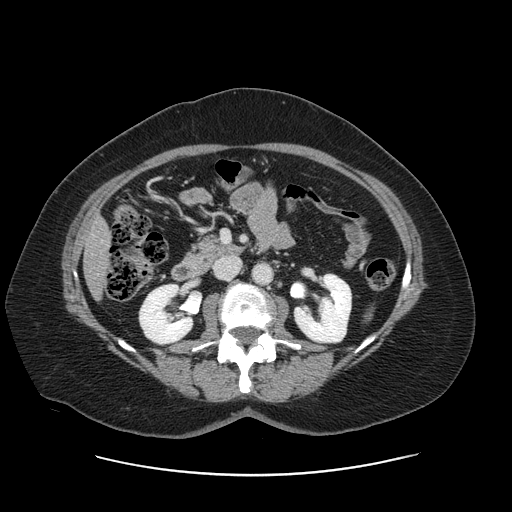
Contrast-enhanced abdominal CT, one axial slice. Slice 50 of 161 in the series (ordered by position). 120 kVp. Intravenous contrast given. Soft-tissue window (W 400 / L 40 HU). 2.5 mm slice thickness. 512 × 512 image matrix. Female patient, age 62 years. From the clinical record (not read from this slice): diagnosis: colorectal cancer liver metastases, imaged before liver resection; multiple liver metastases: no; largest metastasis: 2.5 cm; disease in both lobes: no.
Structures marked on this image (expert manual segmentation):
- liver: bounding box (x1, y1, x2, y2) in pixels: (85, 219, 110, 295)